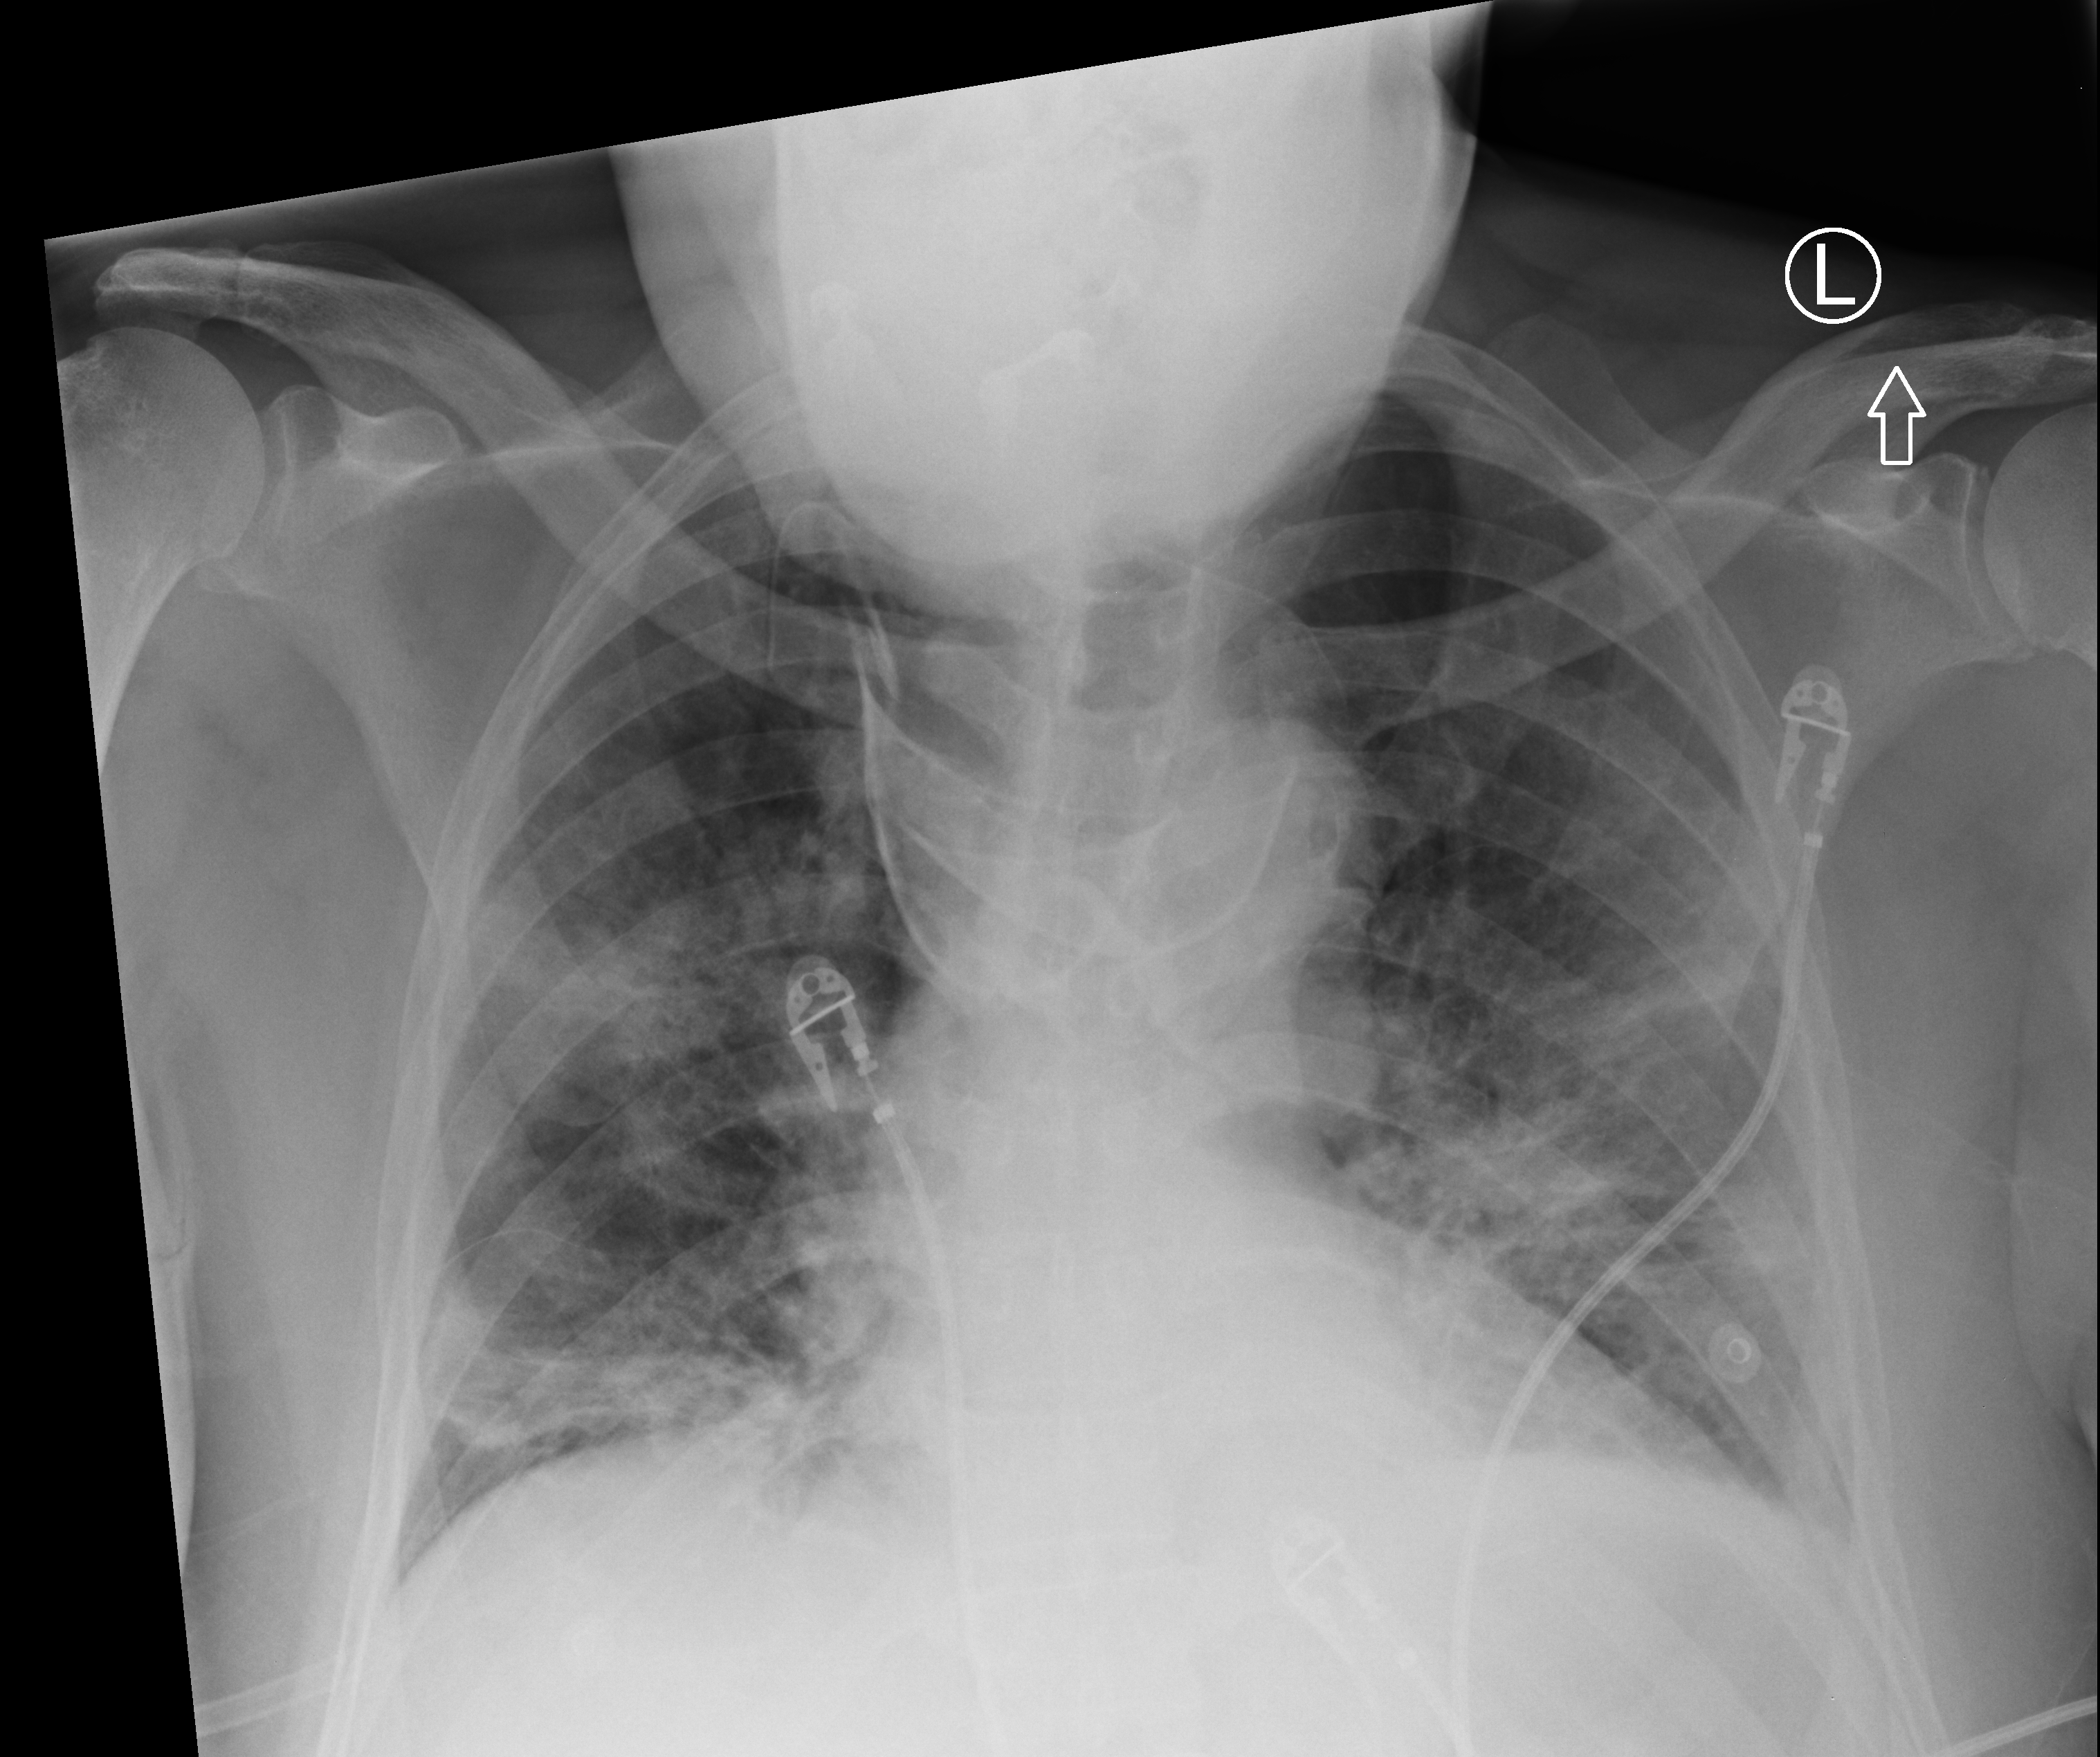
Bedside chest radiograph (computed radiography), anteroposterior (AP) projection. Patient hospitalised with COVID-19; male, aged 60–74 years.
Hospital-stay facts (about this admission, not read from this image; timing relative to this image not recorded):
- other chronic lung disease (admission record): no
- COPD (admission record): no